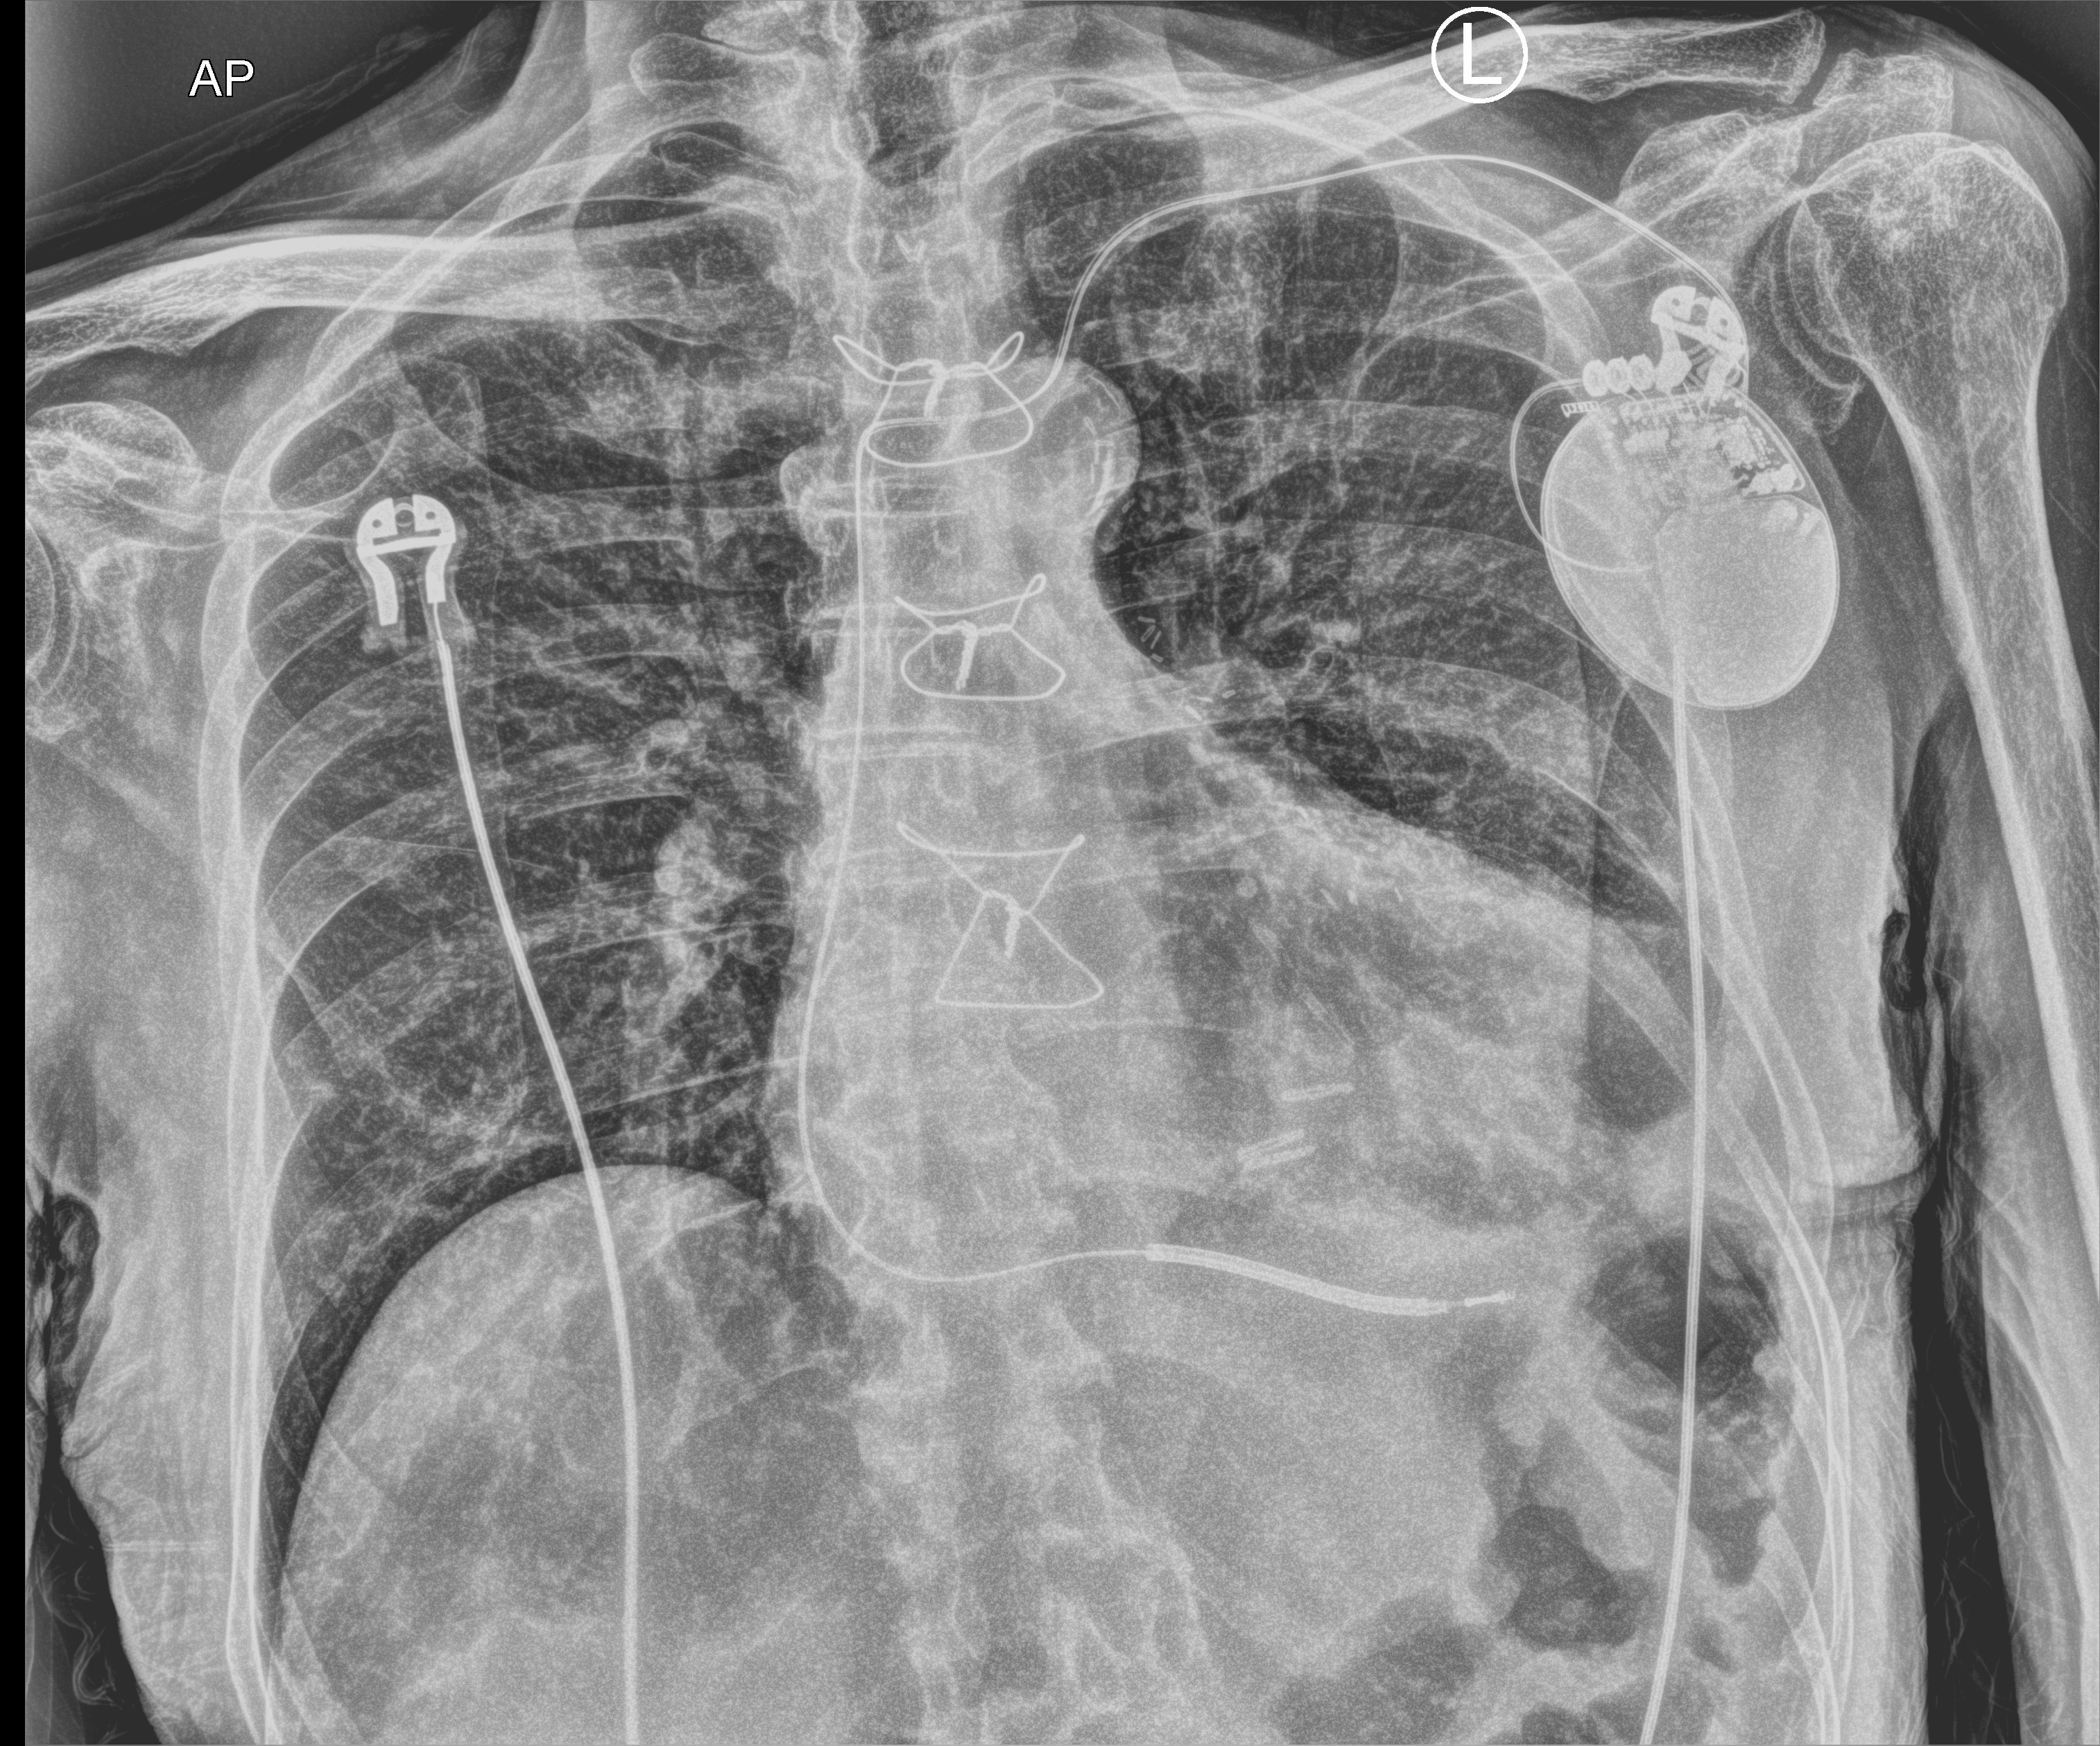
Portable chest radiograph. Patient hospitalised with COVID-19; male, aged 75–90 years.
From the hospital-stay record, not from the radiograph (when in the stay this image was taken is not recorded):
- length of hospital stay: 25 days
- mechanically ventilated during this hospital stay: no
- admitted to intensive care during this hospital stay: no